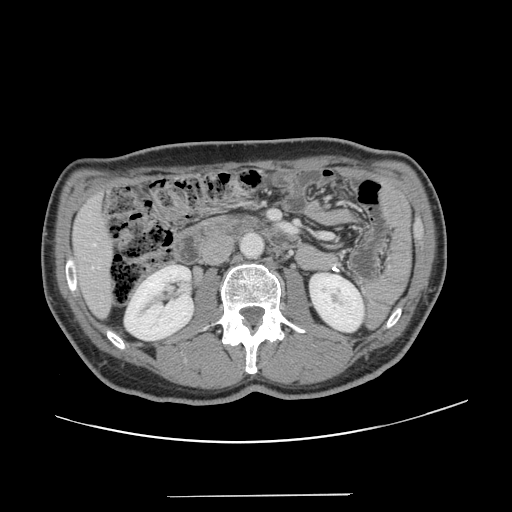
Contrast-enhanced abdominal CT, one axial slice. 120 kVp. Intravenous contrast given. Soft-tissue window (W 400 / L 40 HU). 2.5 mm slice thickness. 512 × 512 image matrix, field of view 403 × 403 mm. Male patient, age 60 years. Case-level facts recorded for this patient, not image findings: diagnosis: colorectal cancer liver metastases, imaged before liver resection; multiple liver metastases: no; largest metastasis: 2.5 cm; chemotherapy before resection: no.
Outlined on this slice (expert manual segmentation):
- hepatic veins: bounding box <92,244,95,269> (left, top, right, bottom; pixels)
- liver: <75,198,111,315>
- planned liver remnant (the part of the liver to remain after resection): <75,198,111,315>